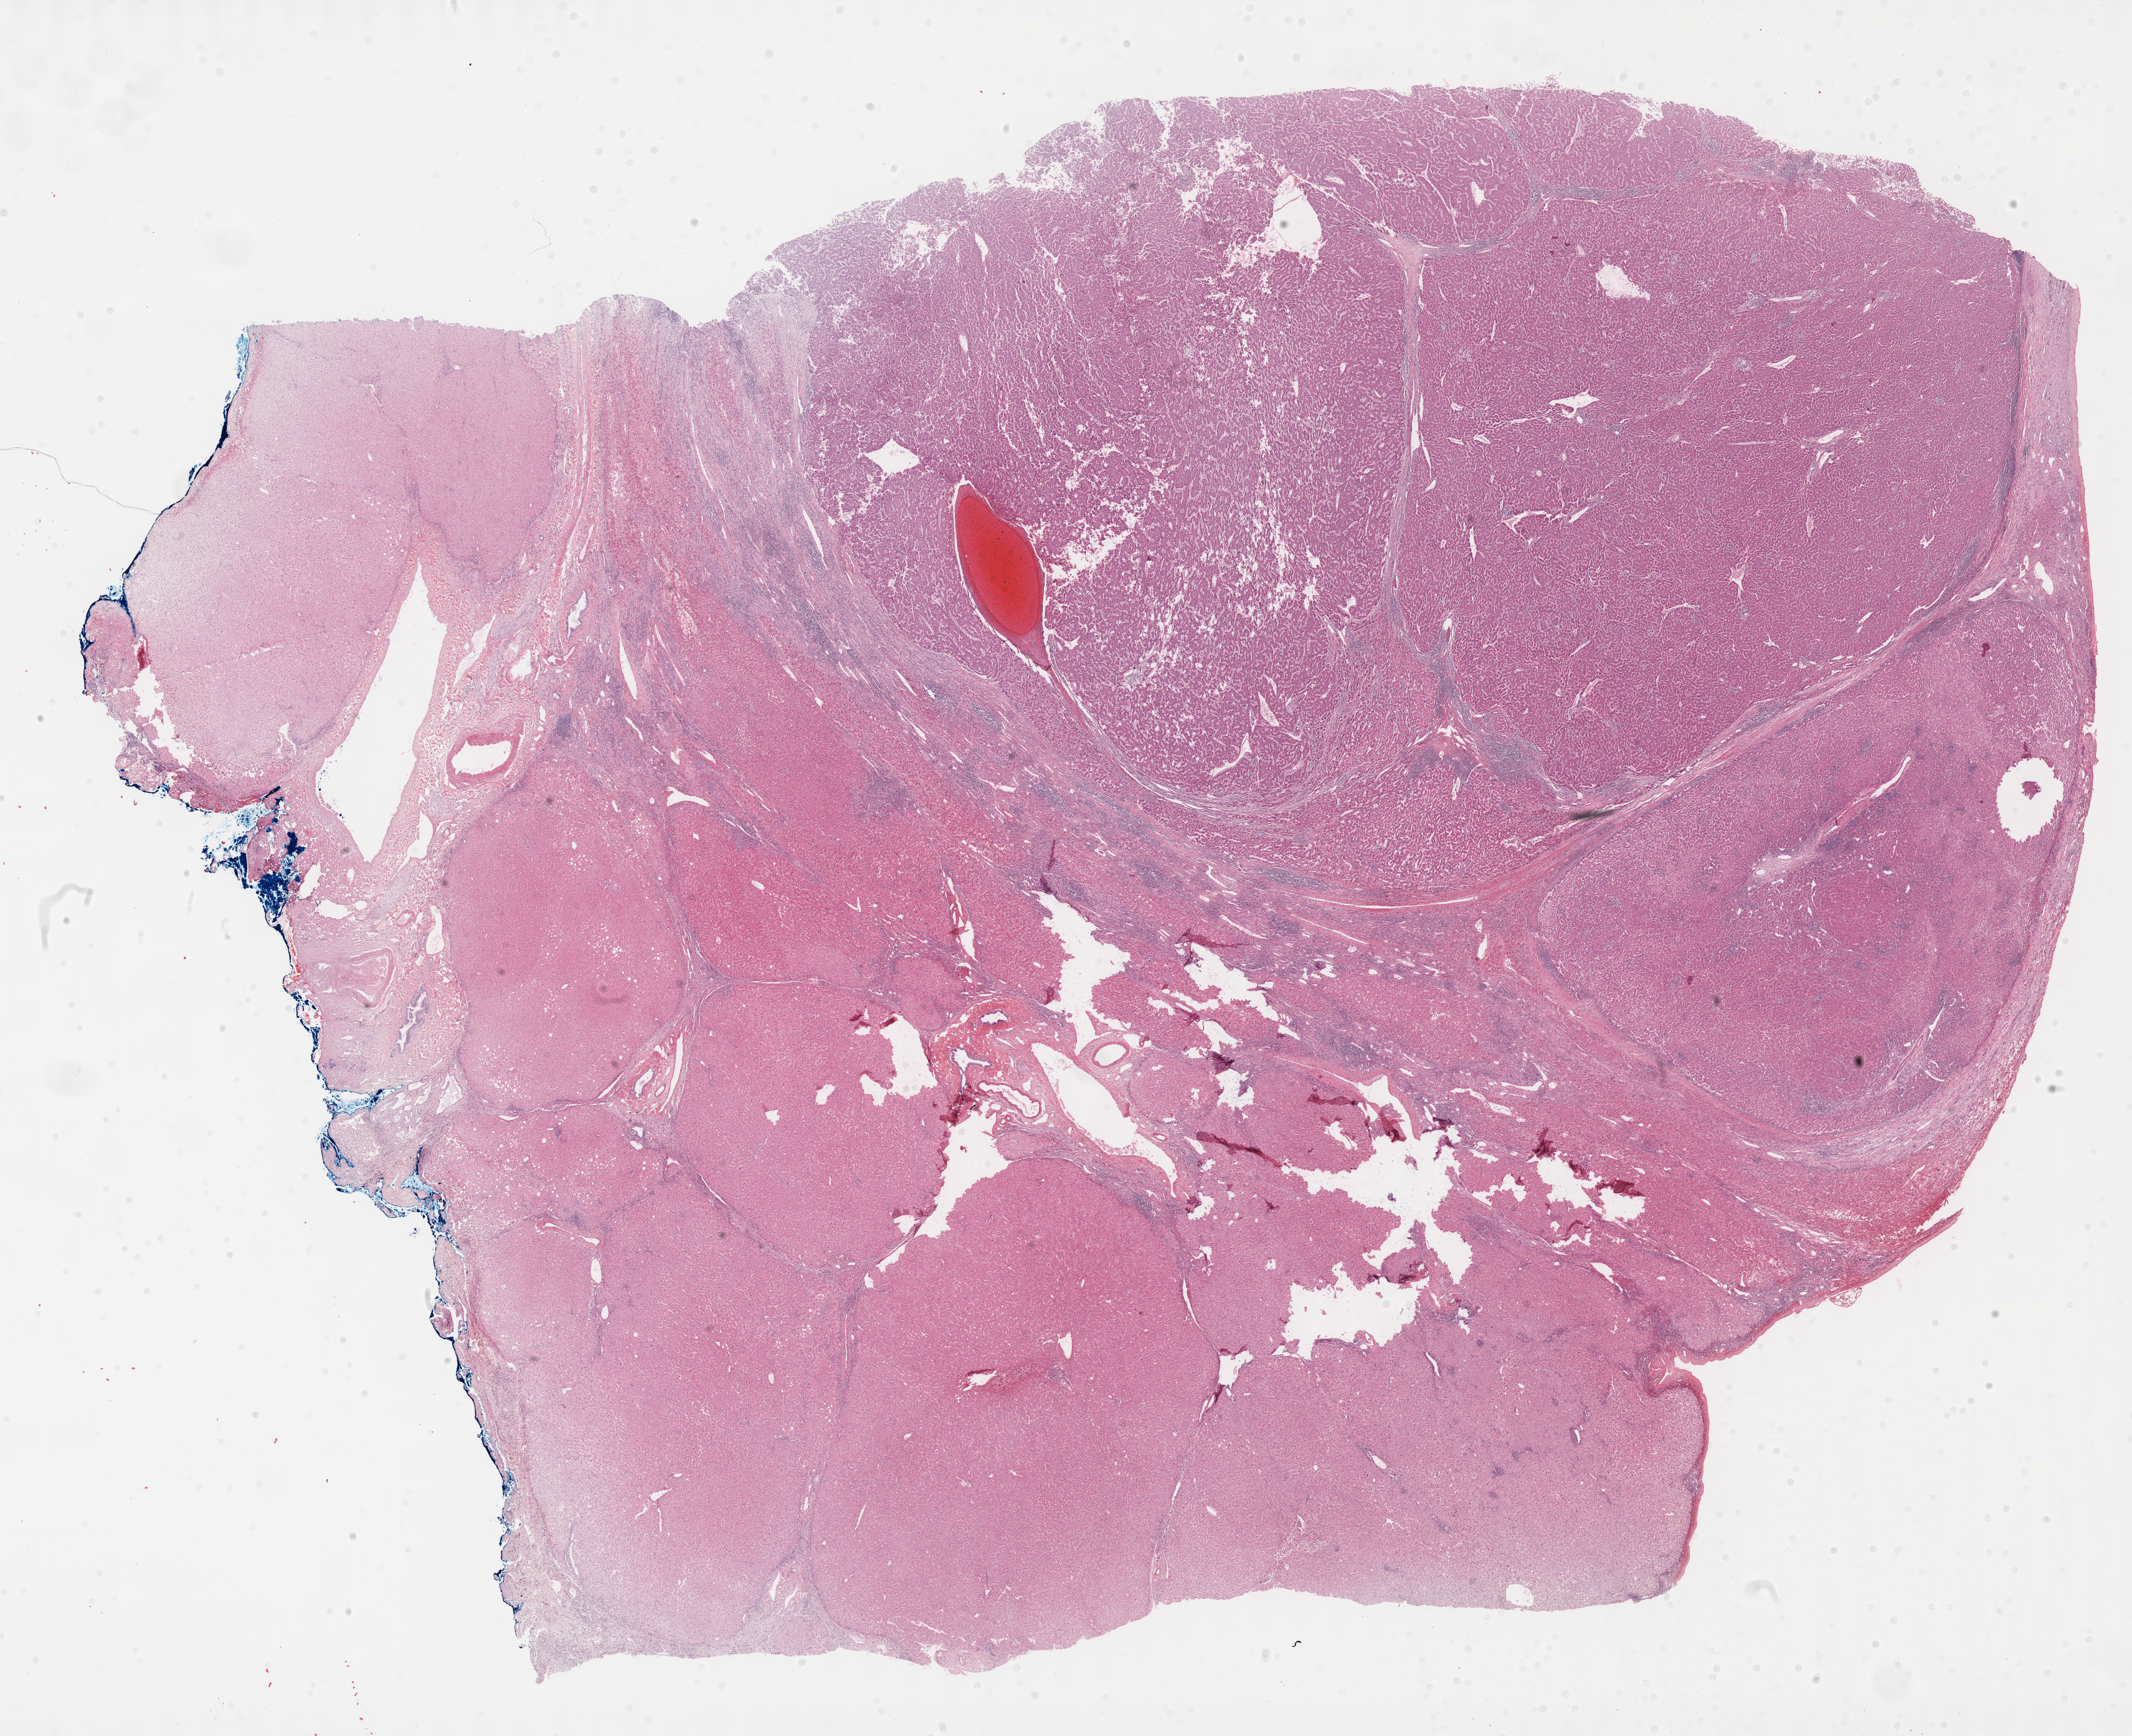
Hematoxylin and eosin (H&E) stained whole-slide image — low-resolution overview of the scanned area, about 27.7 x 22.5 mm (from a 40x scan); FFPE section; sample: primary tumour, liver. Female, age 47 years at initial diagnosis. Histologic grade: G3 (poorly differentiated).
AJCC pathologic stage: I (7th edition). Pathologic diagnosis: Hepatocellular carcinoma, NOS.